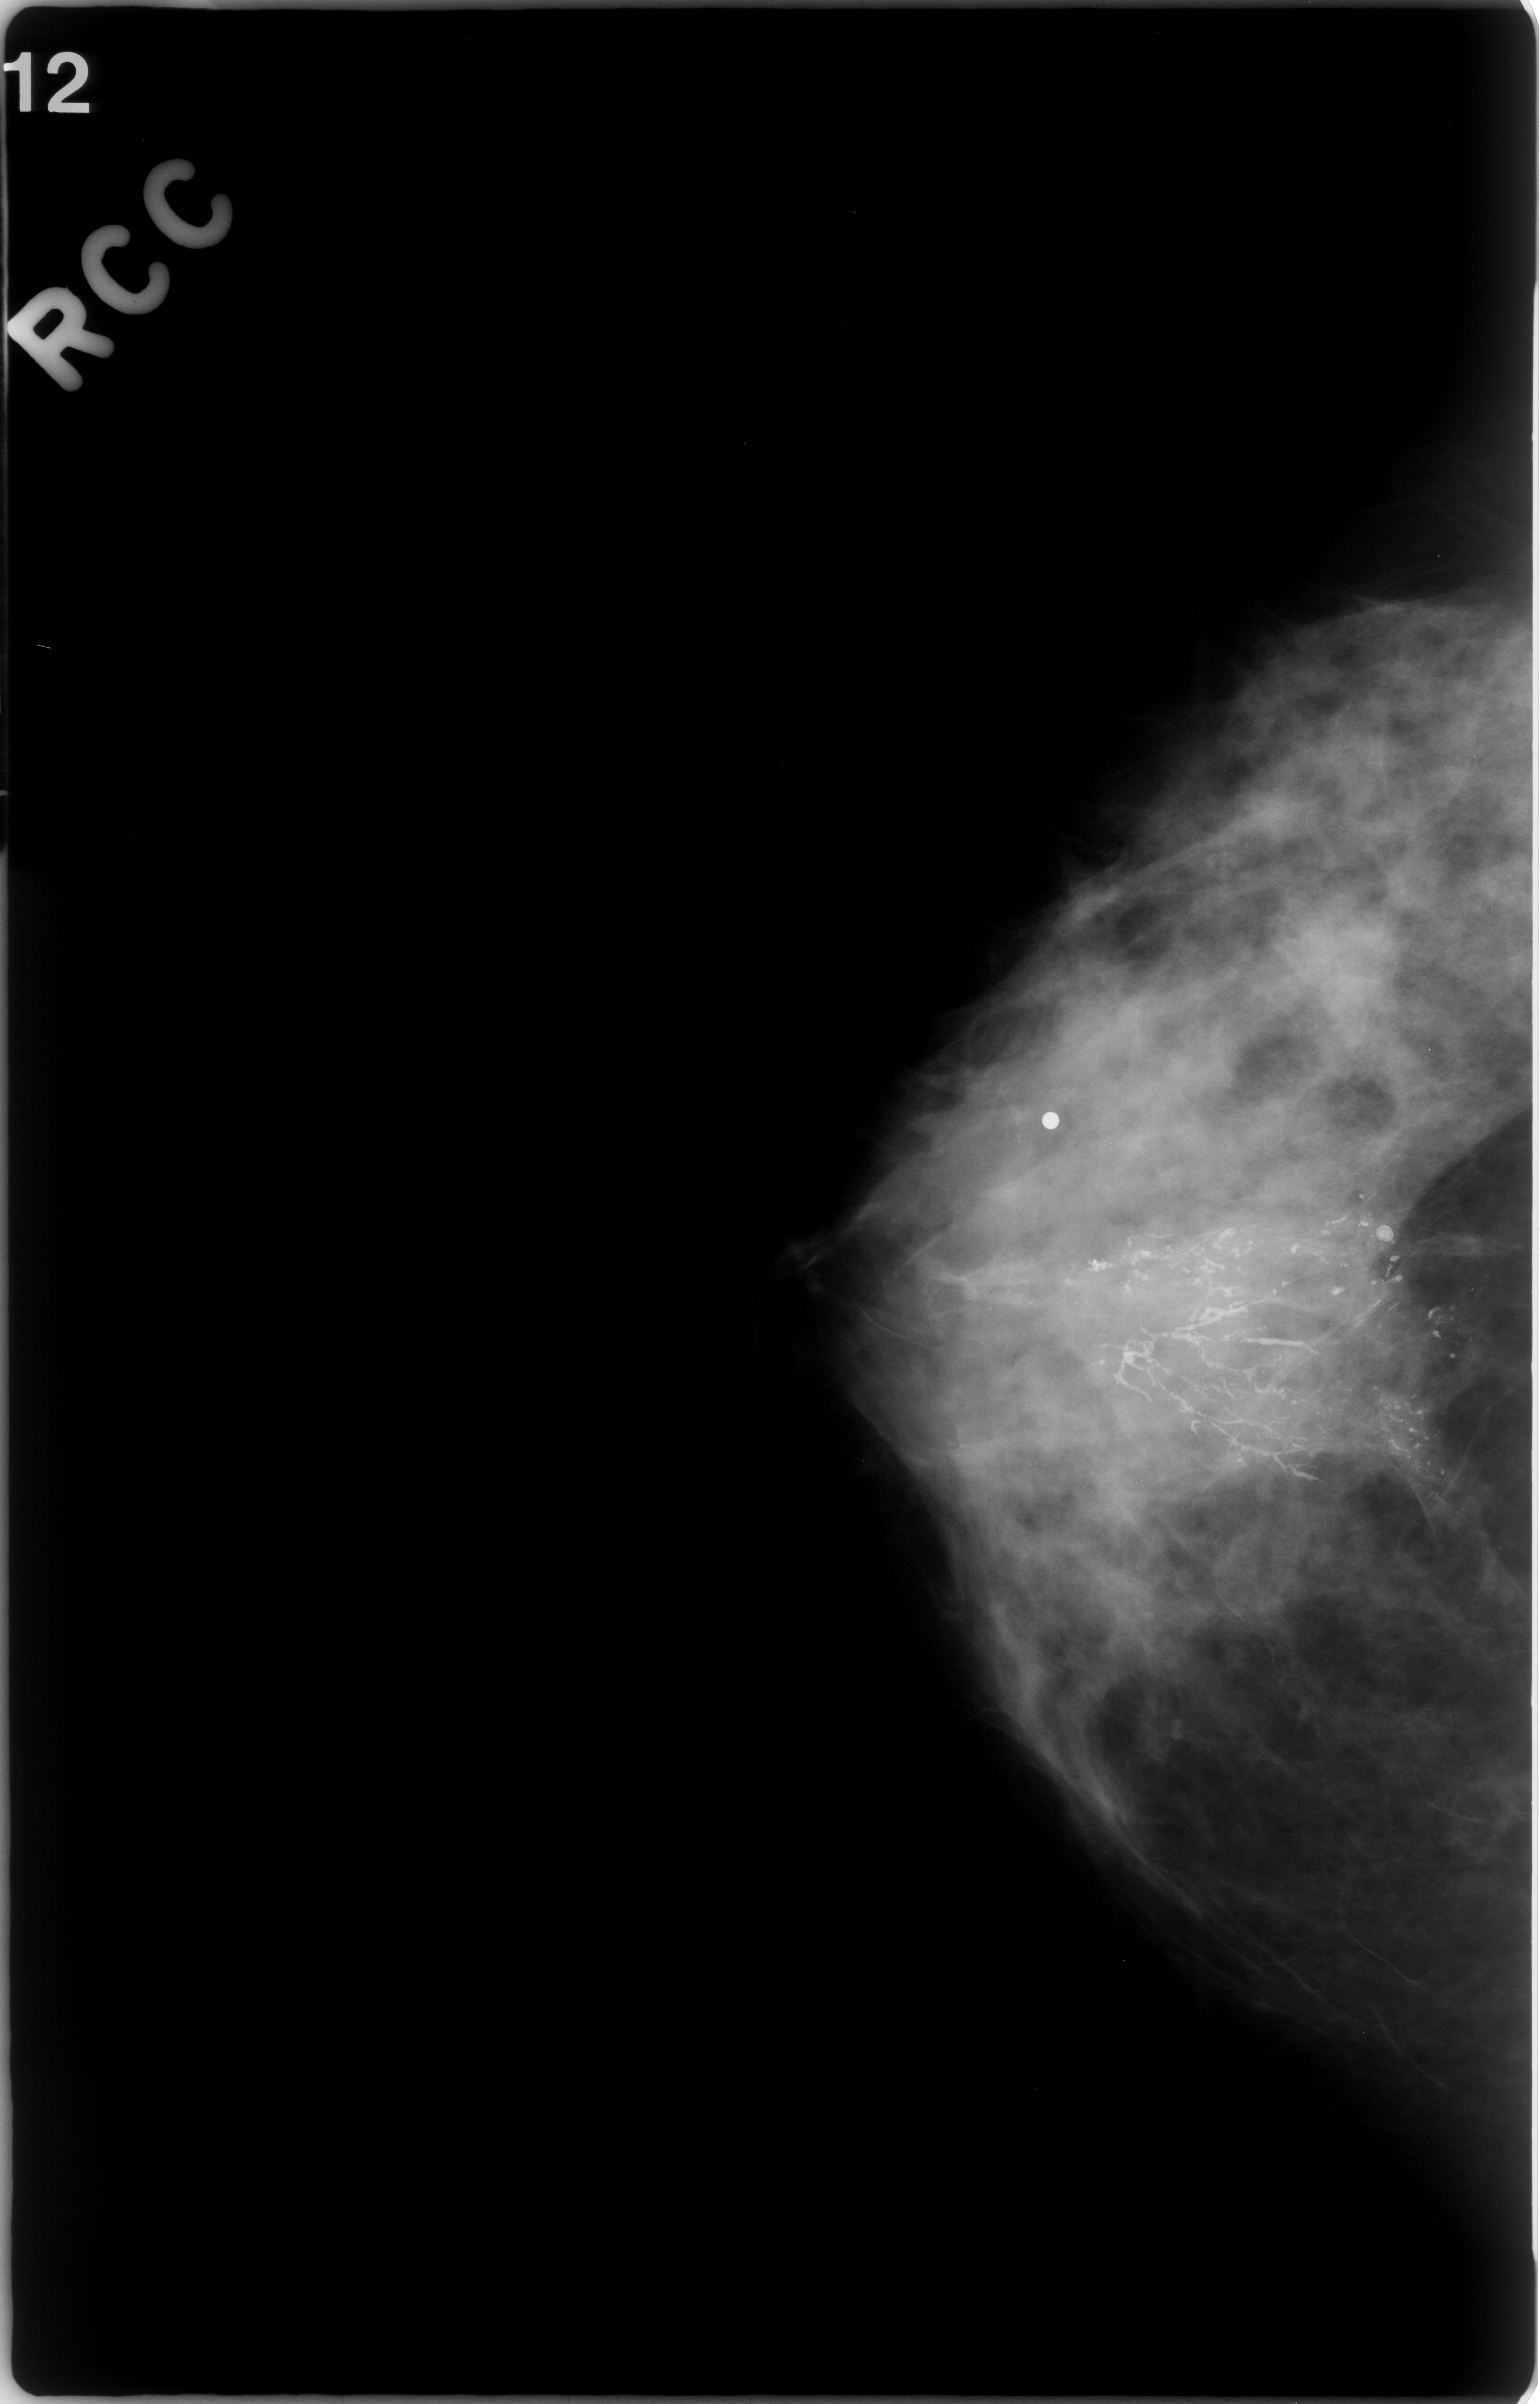
Scanned film-screen mammogram. Right breast. CC view. 1540 × 2404 image matrix.
Expert-marked regions of interest on this image (one box per marked abnormality):
- calcifications, morphology fine linear branching, distribution segmental; BI-RADS assessment category 5; pathology (as recorded): malignant: bounding box (x1, y1, x2, y2) in pixels: (1000, 1067, 1516, 1504)